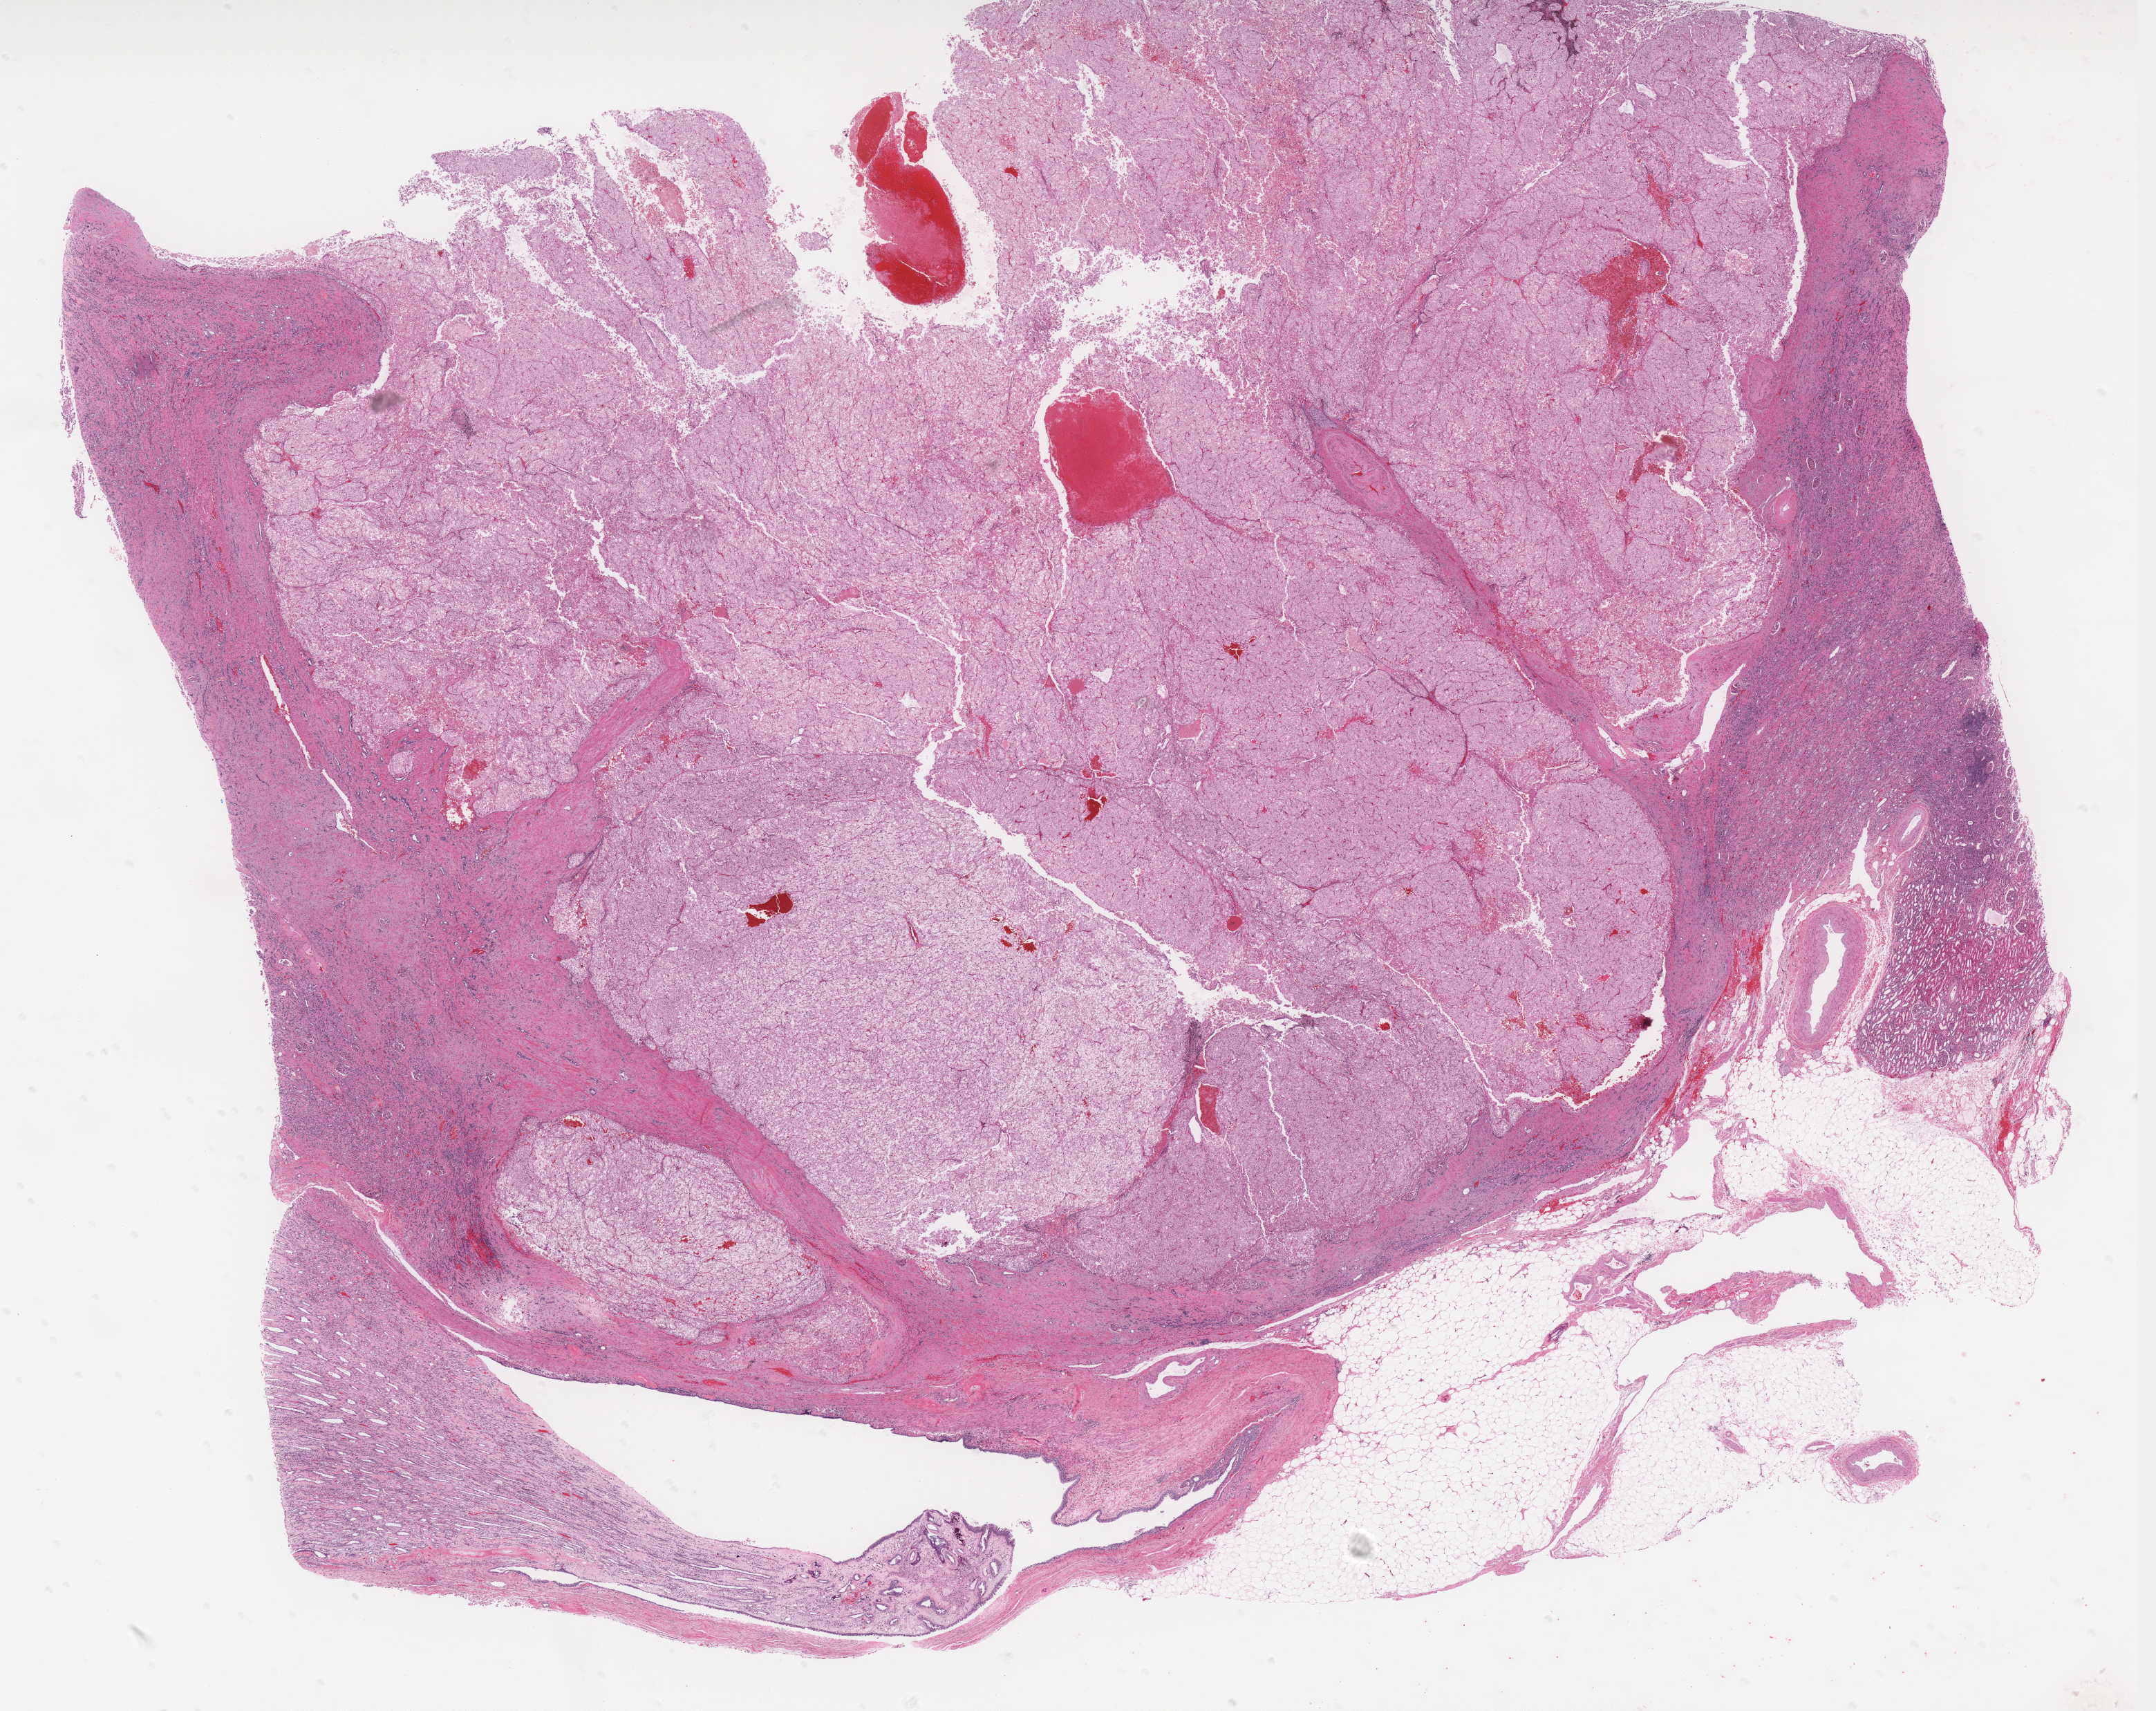
Digitized H&E-stained tissue section (whole slide) — low-resolution overview of the scanned area, about 24.9 x 19.8 mm (acquisition: 40x scan); formalin-fixed paraffin-embedded (FFPE) diagnostic section; primary tumour sample from the kidney. Patient: male, age at initial diagnosis 75 years.
AJCC pathologic stage: III. Histologic diagnosis: Renal cell carcinoma, chromophobe type. Lymph nodes positive (case pathology): 0 of 13 examined.